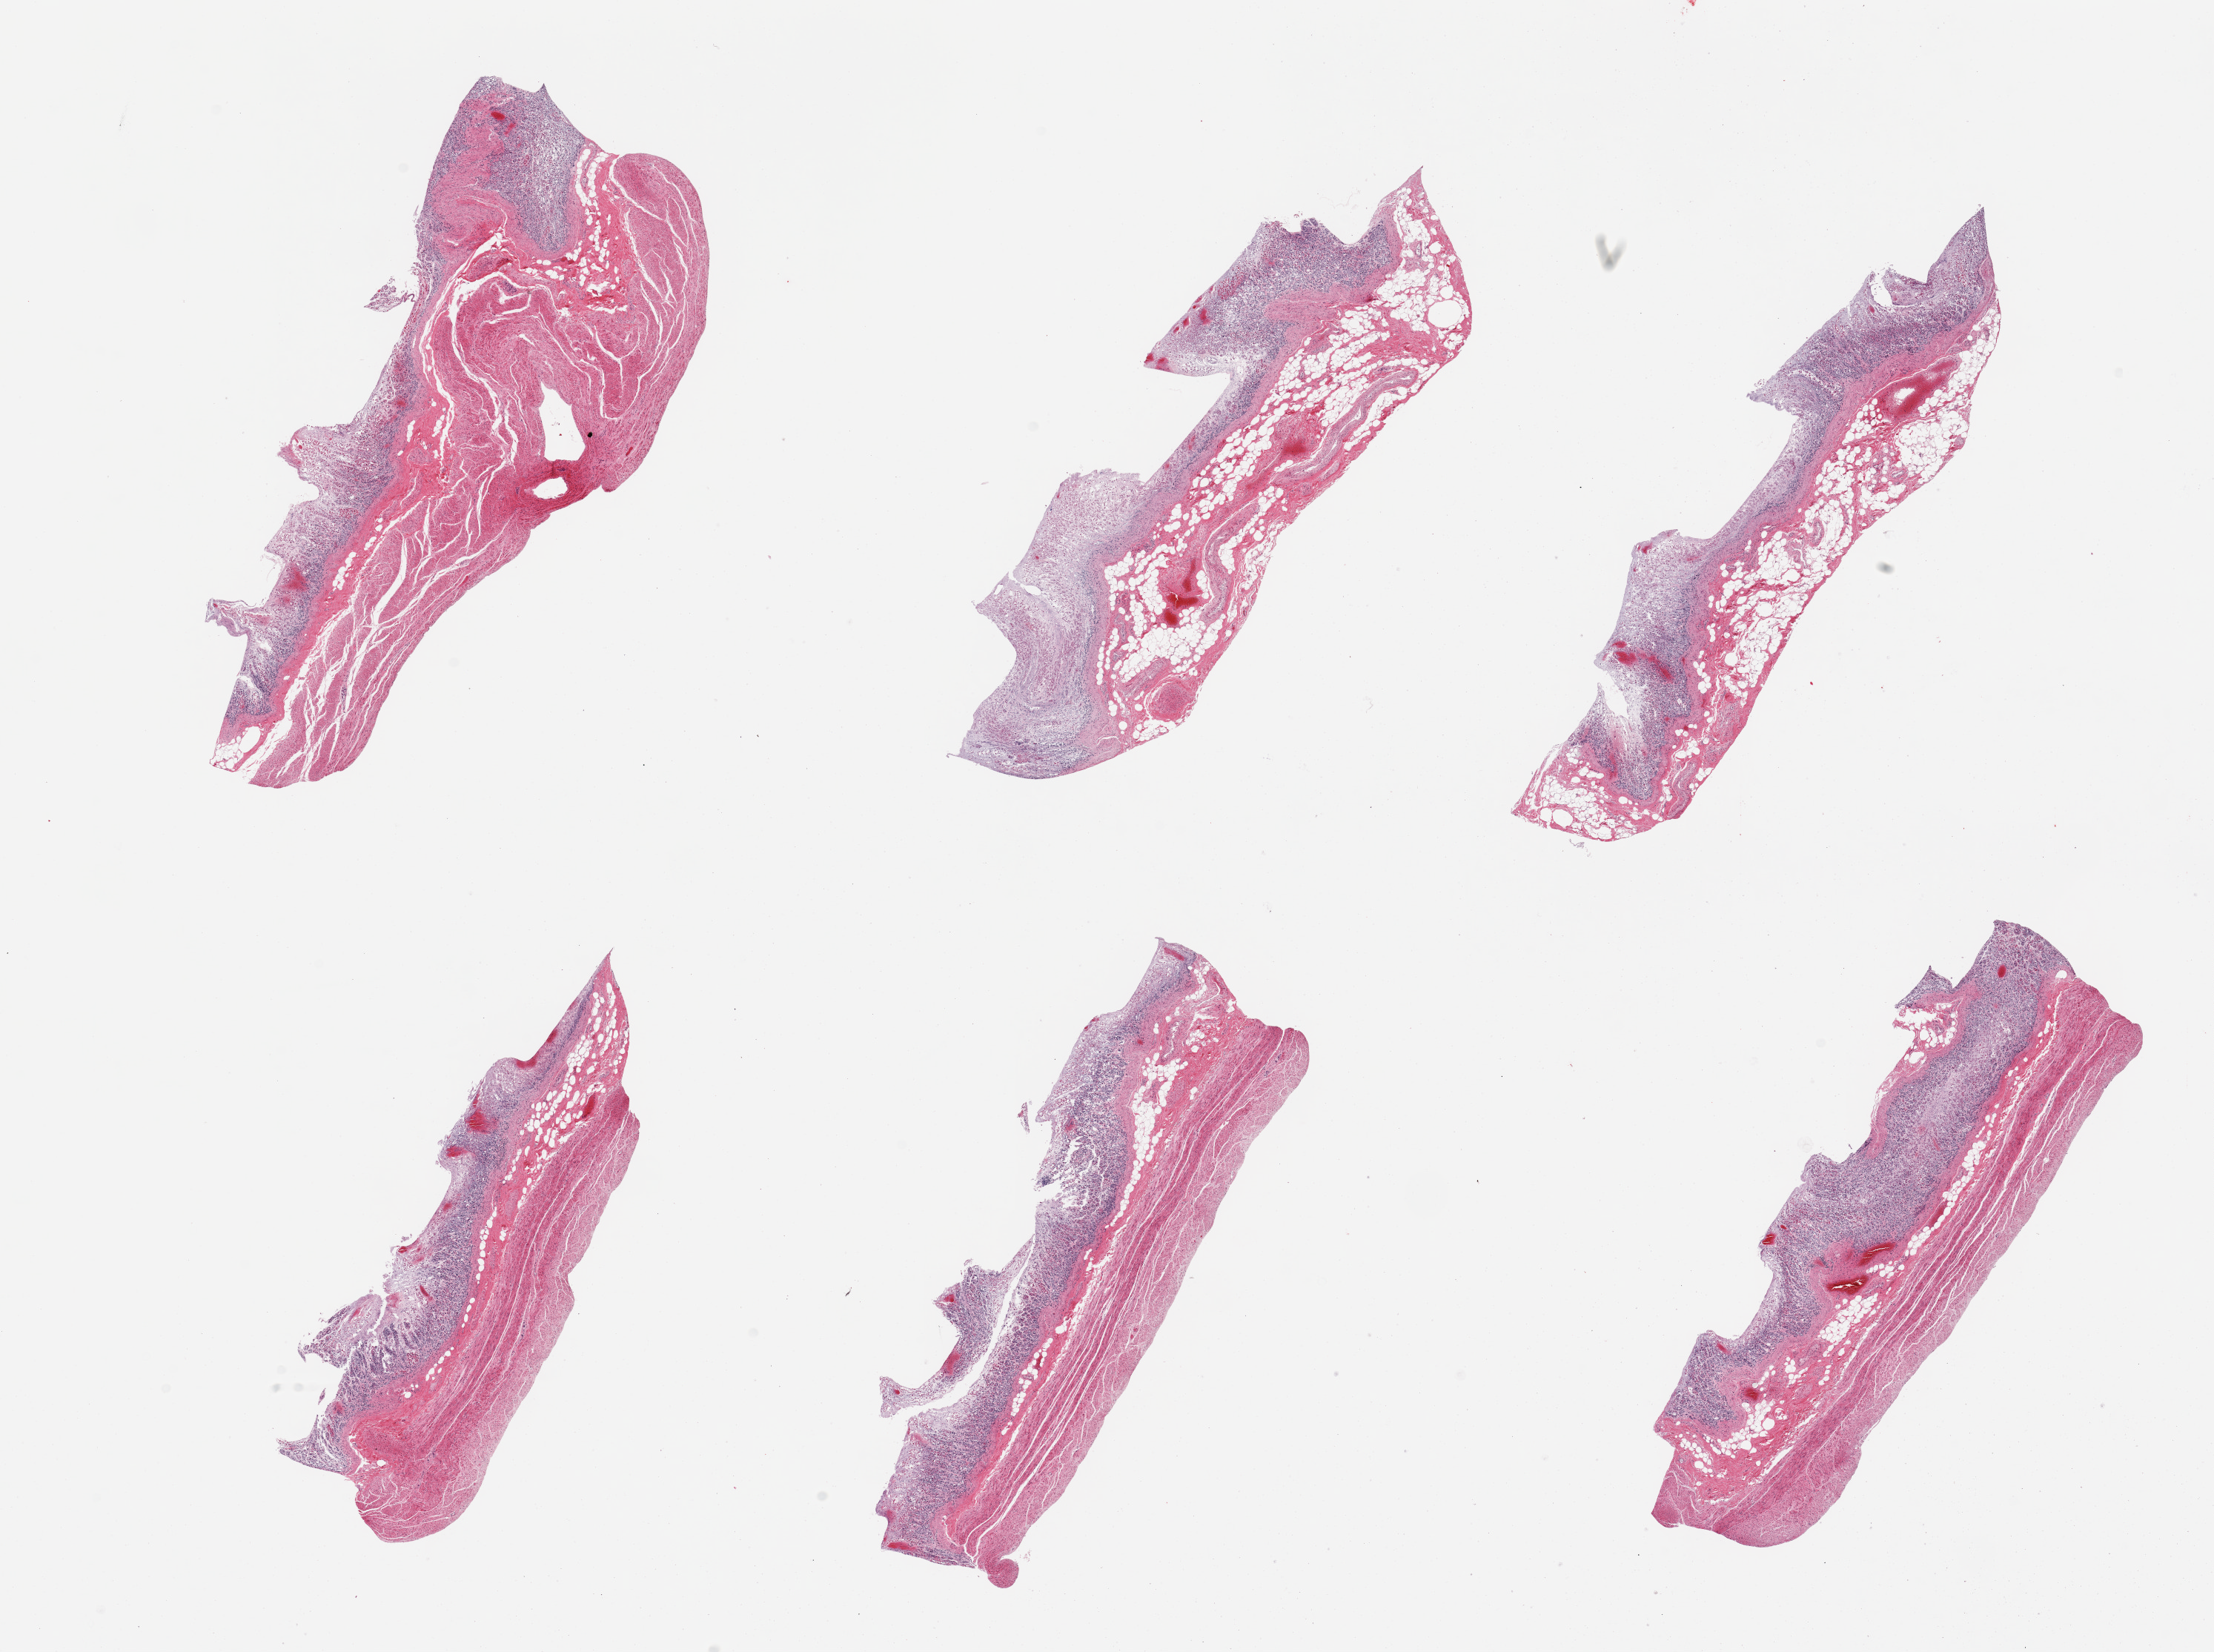
Haematoxylin and eosin whole-slide image, low-resolution overview of the scanned area, about 23.6 x 17.6 mm; PAXgene-fixed, paraffin-embedded tissue; sampled site (target tissue): stomach; donor tissue sample.
• pathologist's review note for this sample: 6 pieces. Mucosa totally autolyzed, muscularis moderate autolysis